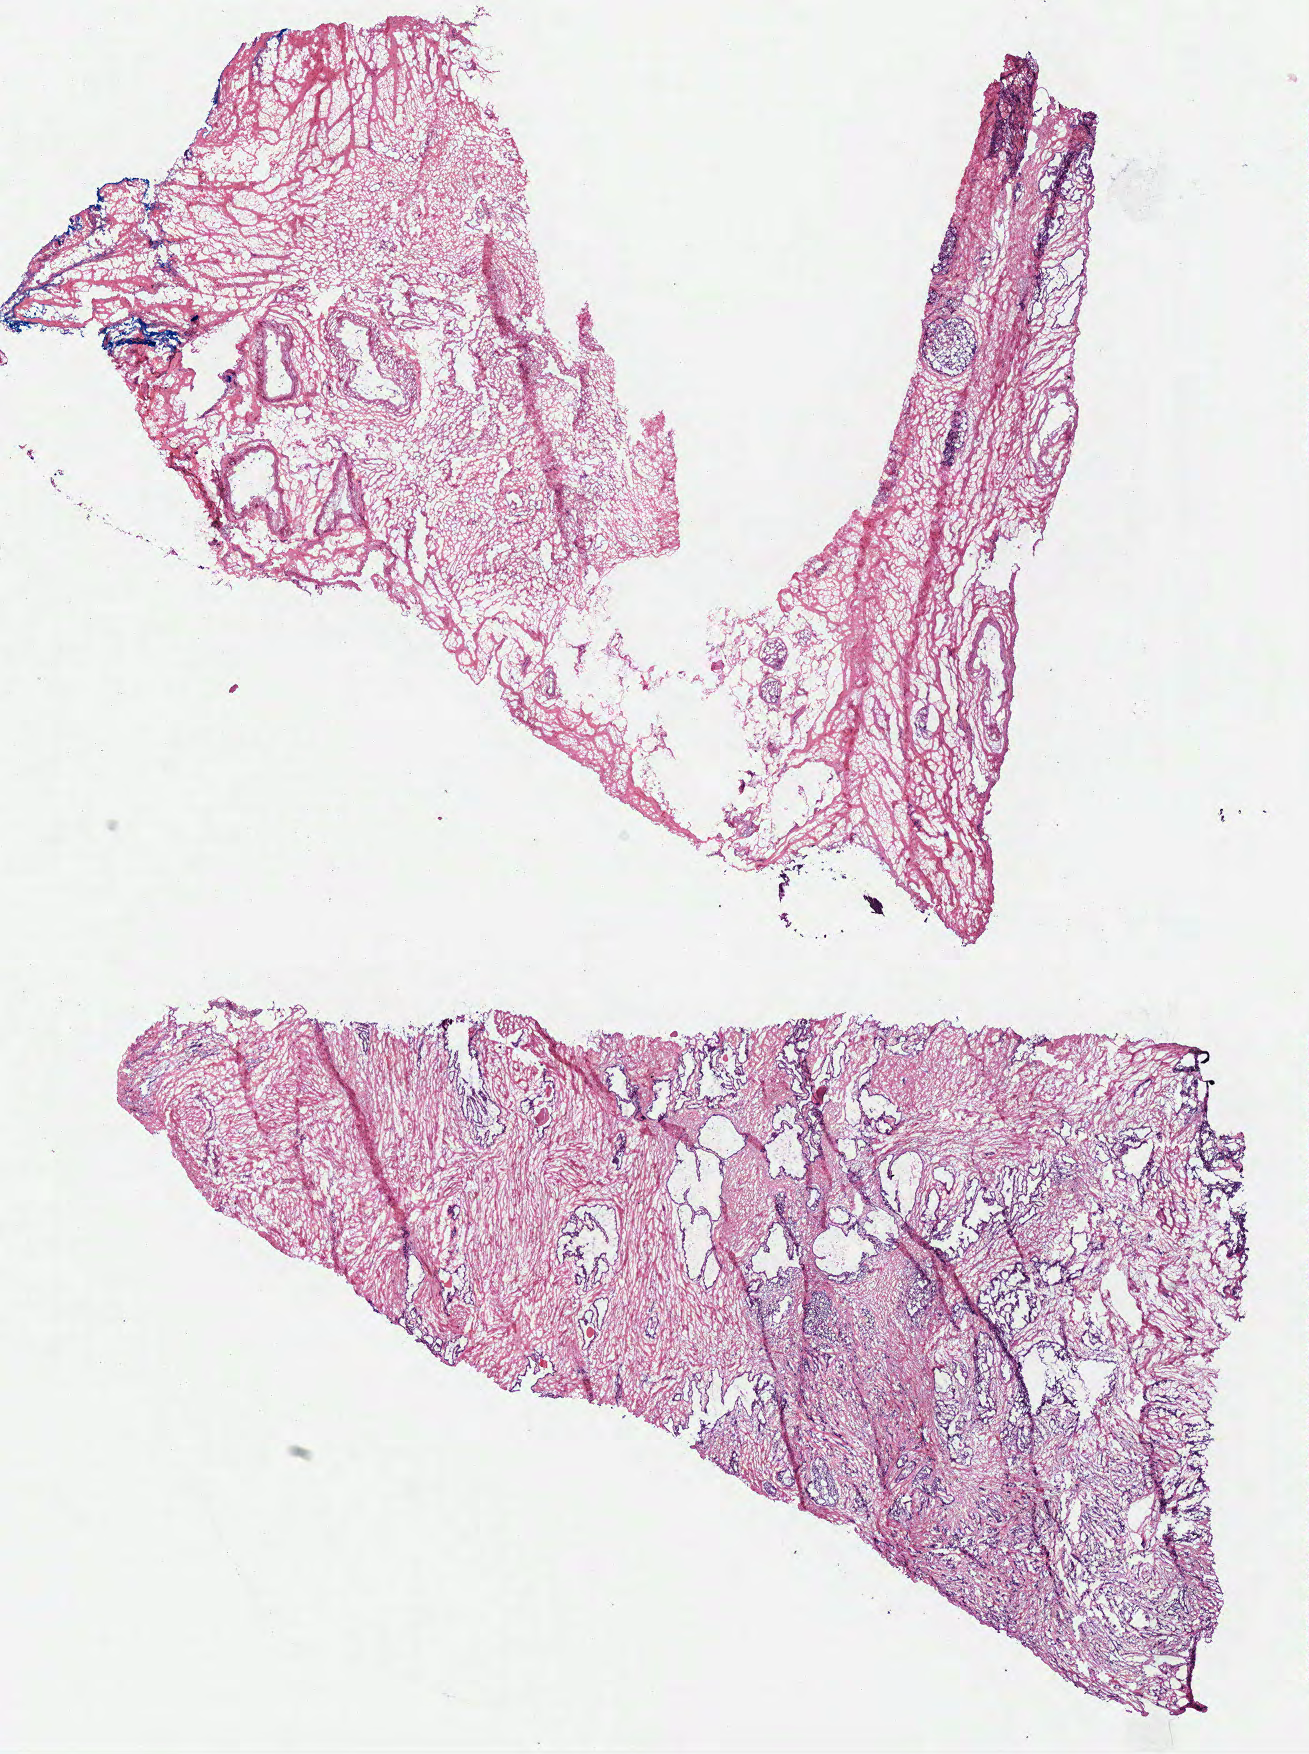
Whole-slide histology image, H&E-stained — a low-resolution overview of the entire scanned area, about 10.3 x 13.8 mm (slide scanned at 40x), frozen section from the bottom of the tissue portion, sample: primary tumour, prostate. Patient: male, age at initial diagnosis 62 years. Gleason score: 9 (4+5). Slide review estimates, as recorded: tumour cells 40%, tumour nuclei 55%, normal cells 0%, stromal cells 60%, necrosis 0%.
* diagnosis: Acinar cell carcinoma (prostate gland)
* lymph nodes positive (case pathology): 0 of 9 examined